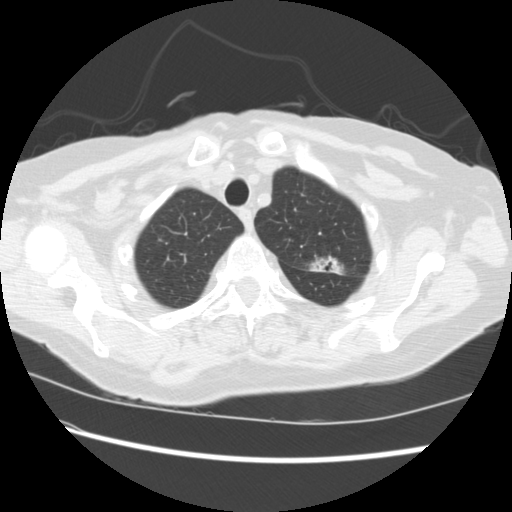
Low-dose screening chest CT, one axial slice; reconstruction kernel STANDARD; 120 kVp; lung window (W 1500 / L -600 HU); 2.5 mm slice thickness; 512 × 512 image matrix.
Structures marked on this image (manually delineated by an expert):
- lesion 1 (tumor, upper lobe of left lung): bounding box (x1, y1, x2, y2) in pixels: (310, 257, 343, 274)